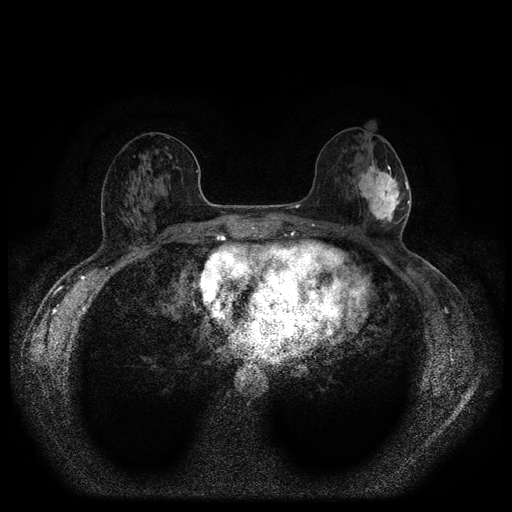
Breast MRI (dynamic contrast-enhanced, multi-phase), one axial slice. Slice 49 of 116 in the series (ordered by position). Dynamic contrast-enhanced series, time point 2 of 5 at this slice position (early post-contrast). 1.5 T. TE 2.7 ms, TR 5.4 ms. 2 mm slice thickness. 512 × 512 image matrix, field of view 330 × 330 mm. Patient: female, 56 years.
Outlined on this slice (semi-automatically segmented with operator editing):
- breast lesion (labelled 'tumour' in the annotation; benign lesions carry a separate 'benign' label): bounding box [x1, y1, x2, y2] px = [355, 153, 405, 227]